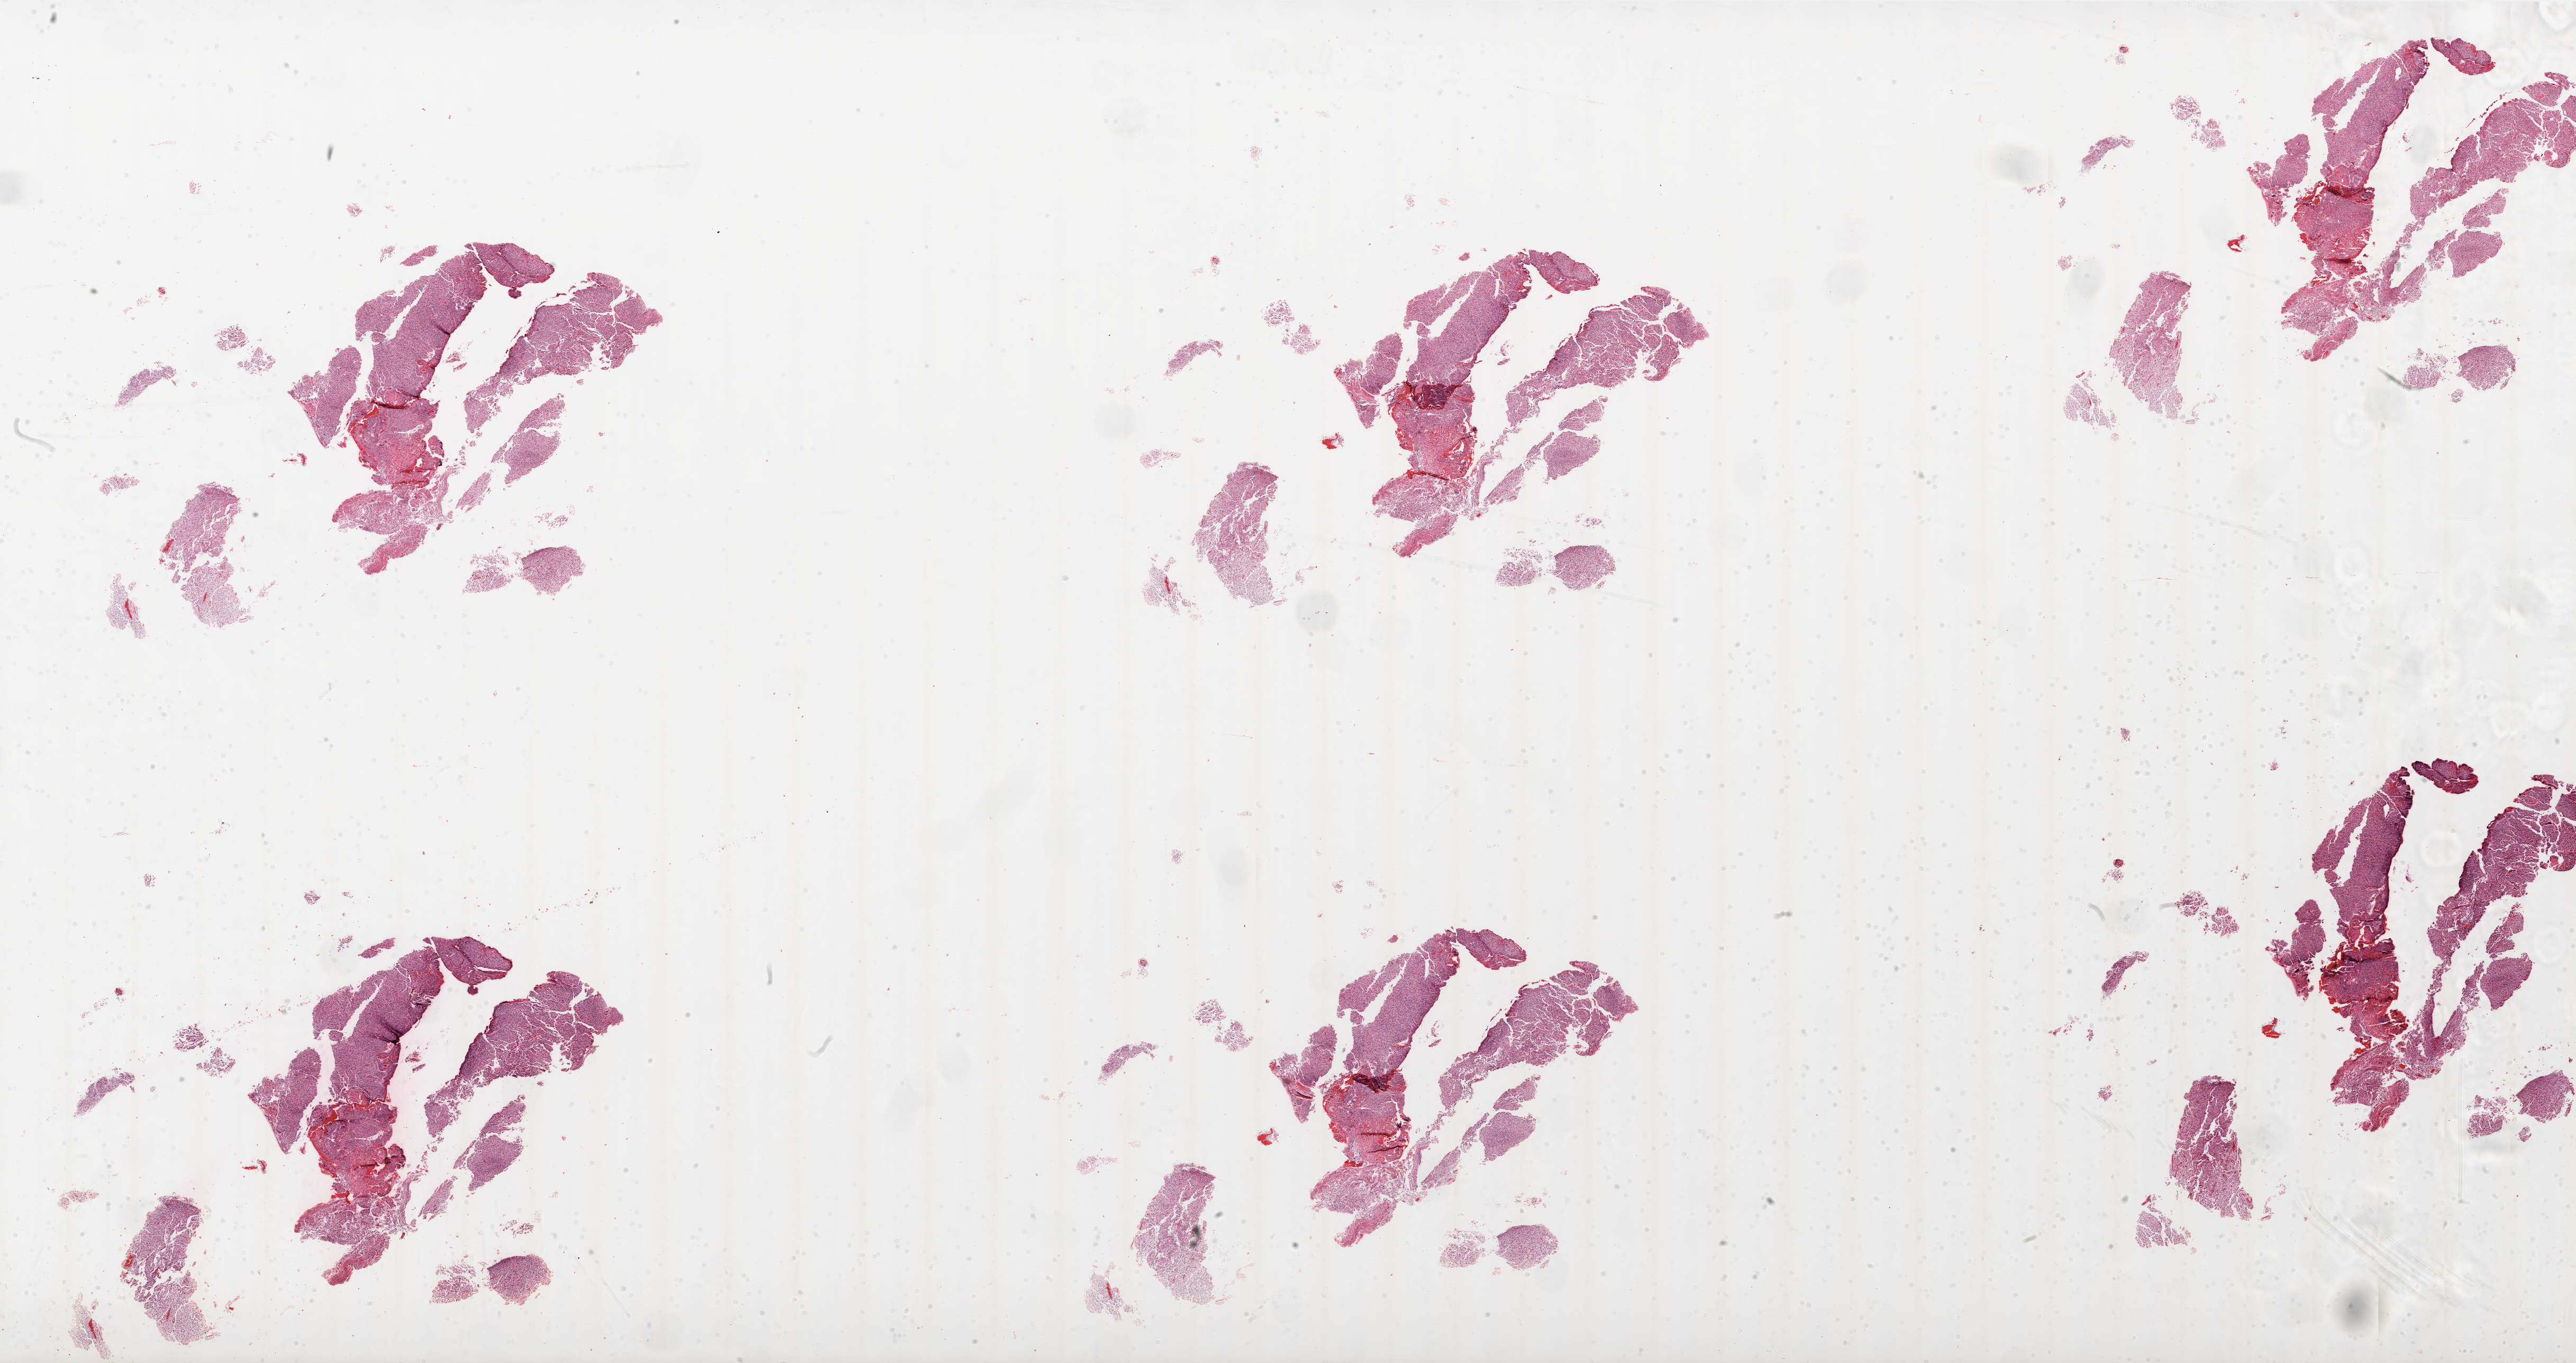
Hematoxylin and eosin (H&E) stained whole-slide image, whole scanned area (about 39.0 x 20.6 mm, slide scanned at 20x) shown as a low-resolution overview, FFPE section, primary tumour sample from the brain. Female patient; age at initial diagnosis 63 years.
- diagnosis: Glioblastoma